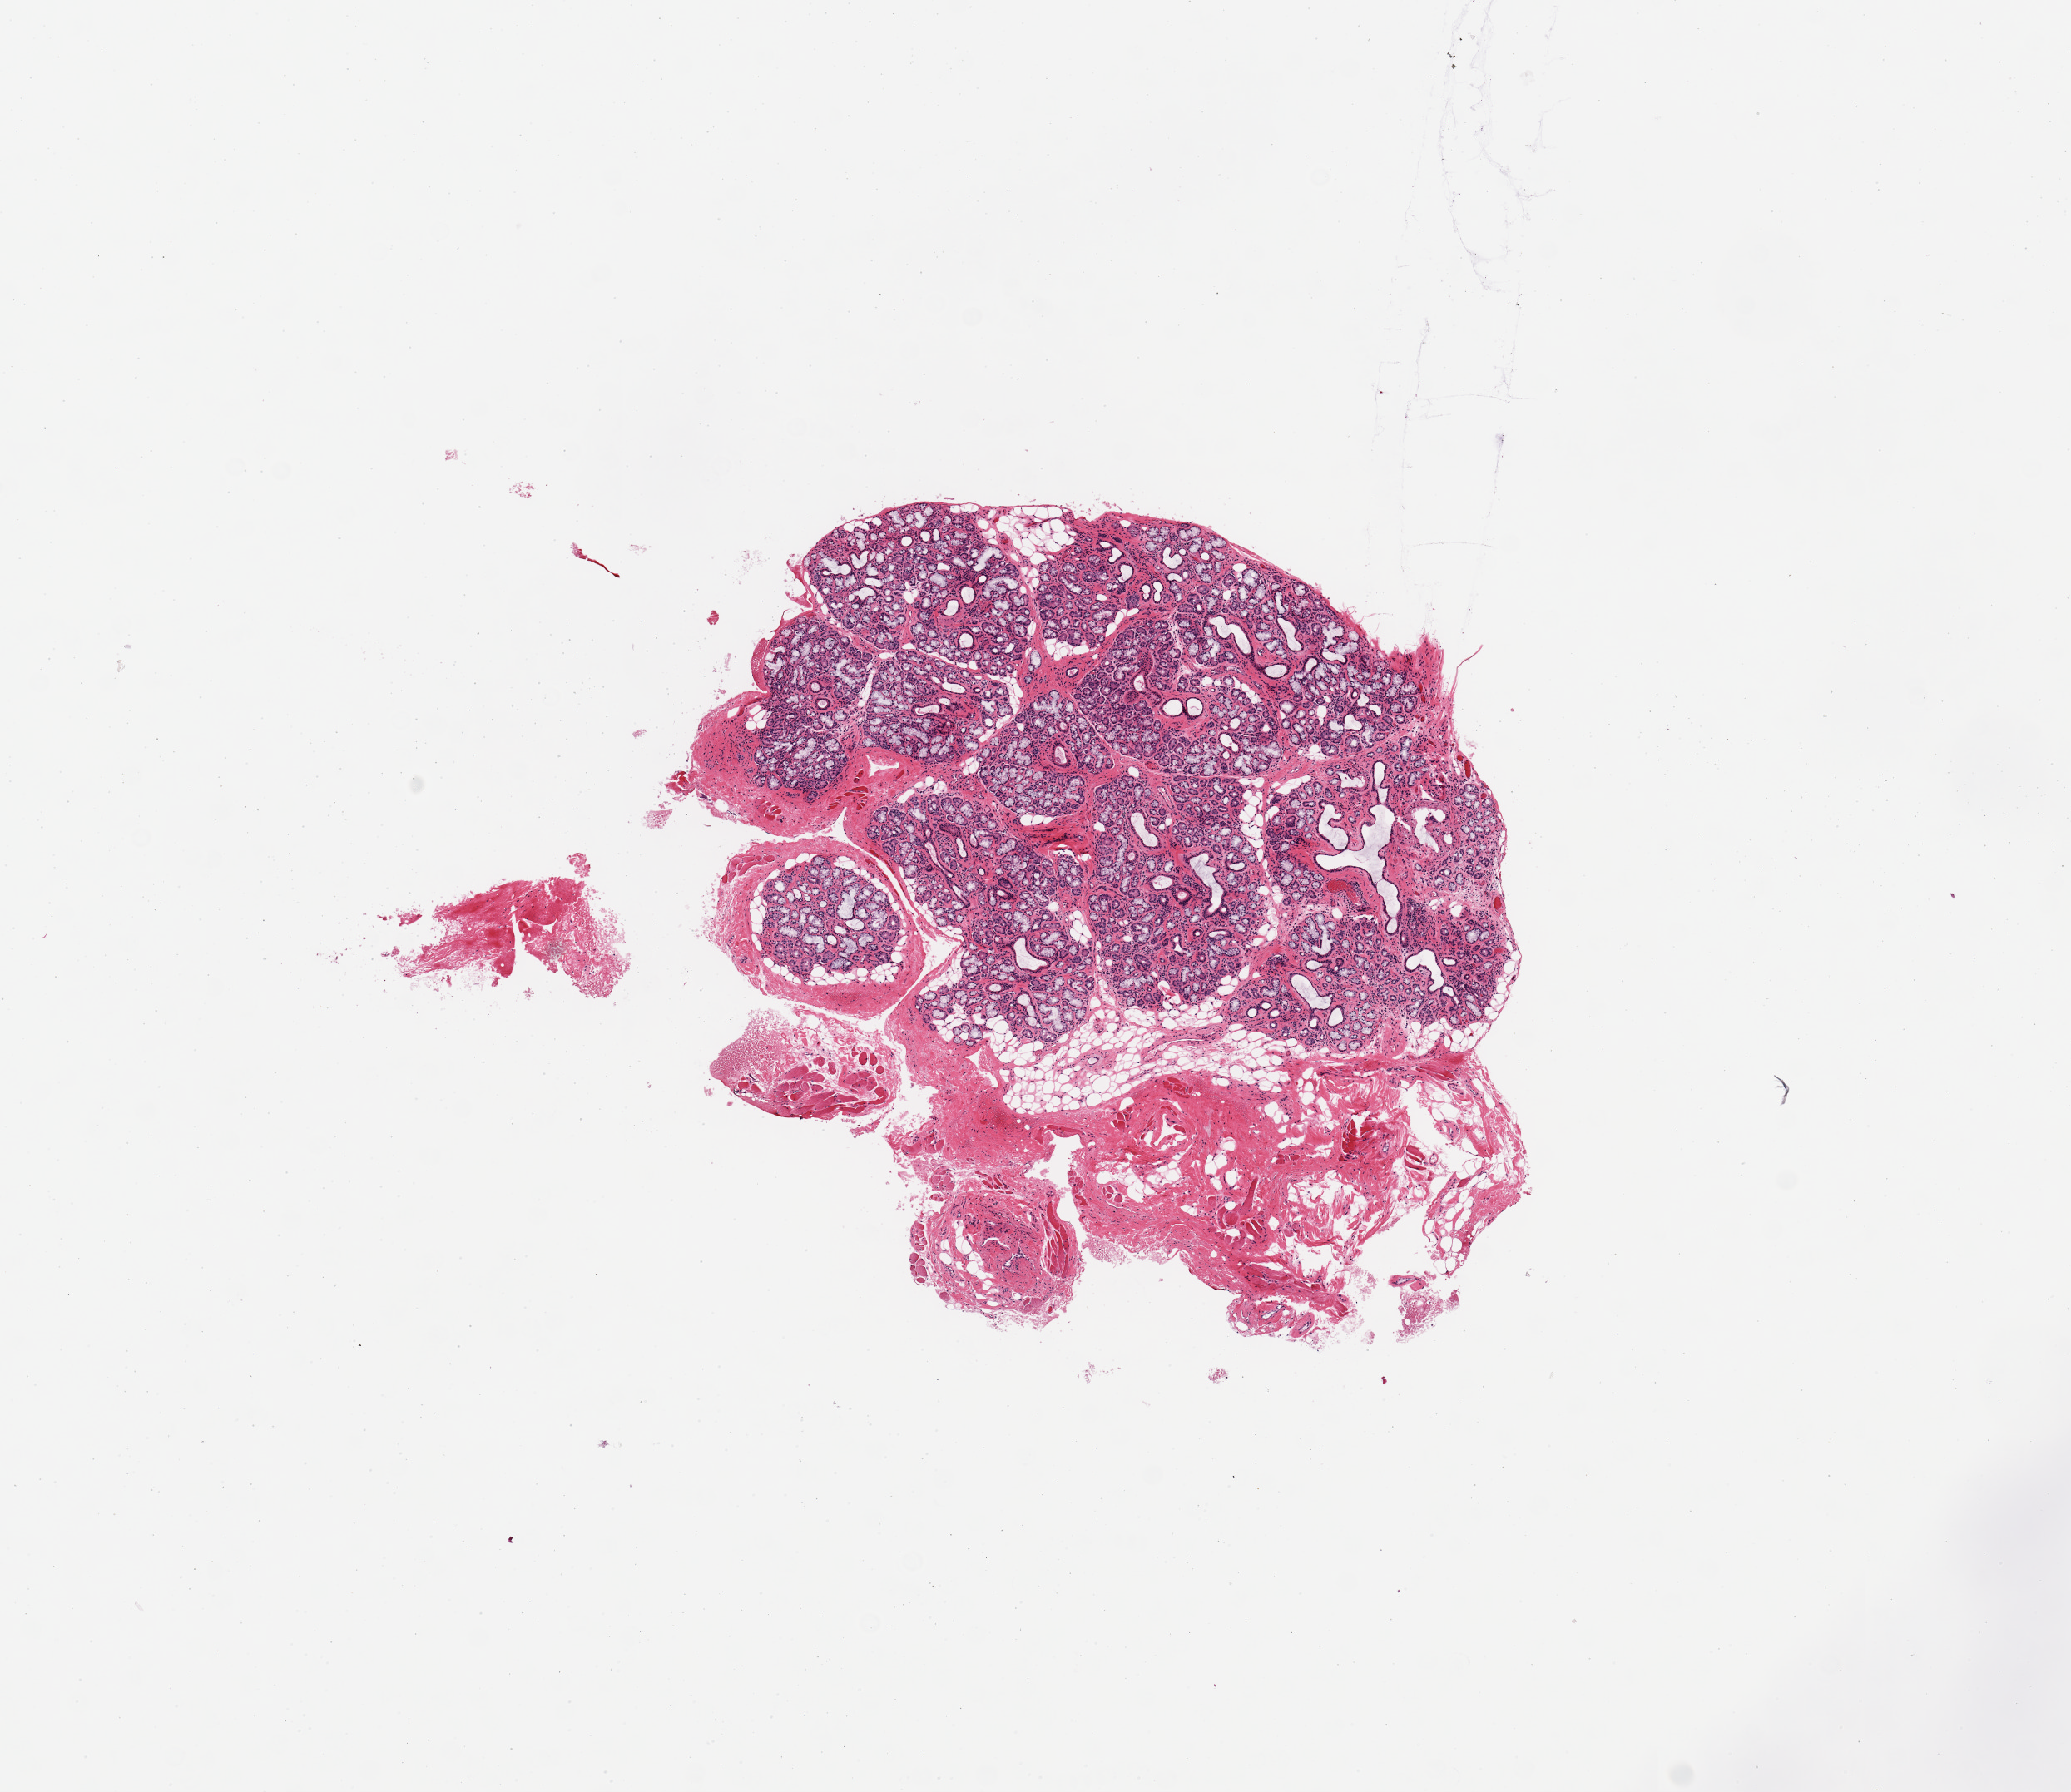
Digitized hematoxylin and eosin (H&E)-stained section — whole scanned area (about 9.8 x 8.5 mm, slide scanned at 20x) shown as a low-resolution overview; PAXgene-fixed, paraffin-embedded tissue; target tissue: minor salivary gland; tissue donor sample. Donor sex: male.
Pathologist's review note for this sample: 1 piece; 60% glandular ductal elements and 40% fibrovascular tissue, fat and muscle.